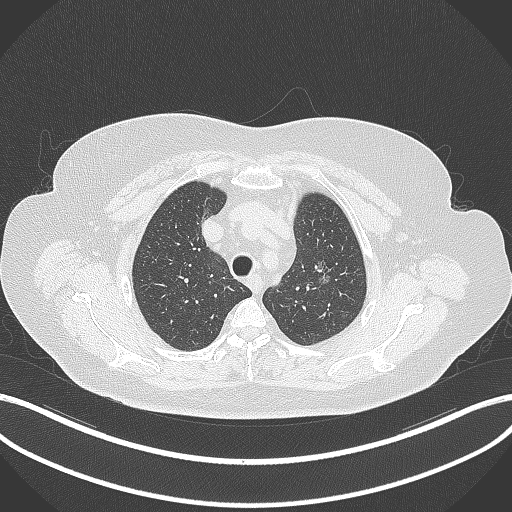
Chest CT, one axial slice. Reconstruction kernel B70f. Lung window (W 1500 / L -600 HU). 1 mm slice thickness. 512 × 512 image matrix. Female patient, age 70 years. Case-level facts recorded for this patient, not image findings: clinical TNM (as recorded): T1c N0 M0.
Outlined on this slice (rectangle marked by the reading radiologist):
- lung tumour (recorded histology: adenocarcinoma): bounding box <312,258,336,289> (left, top, right, bottom; pixels)